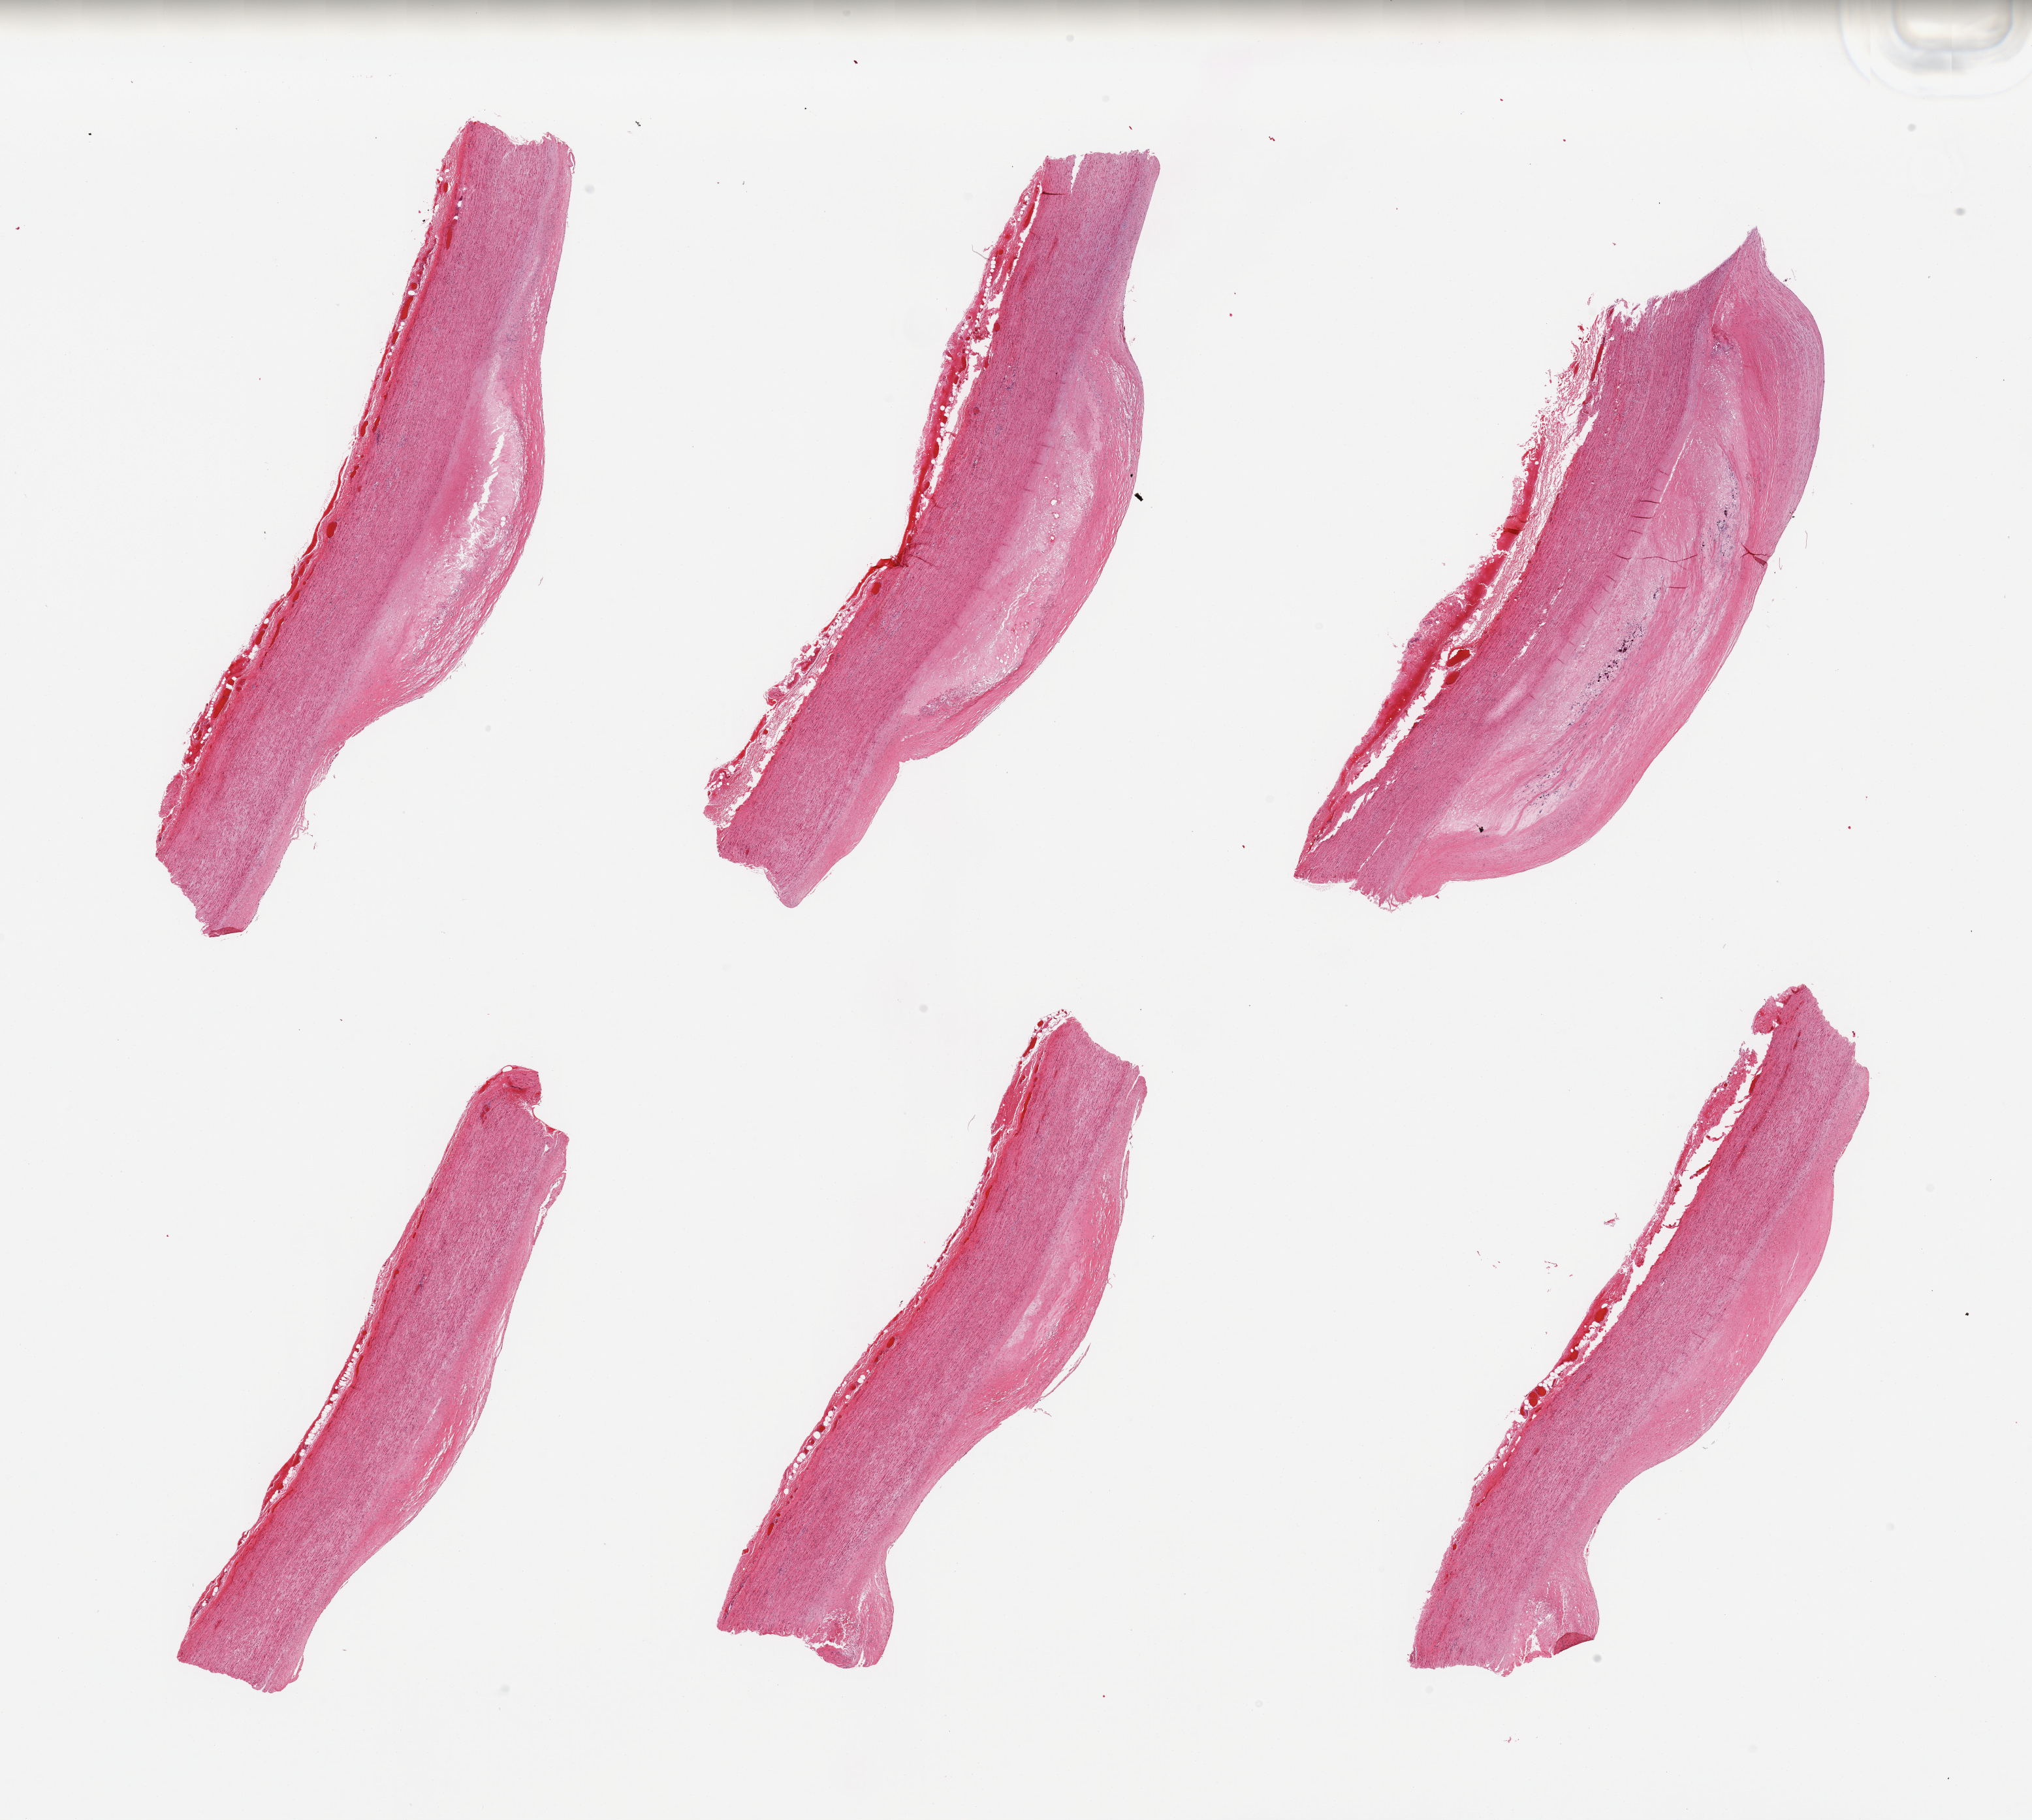
H&E whole-slide image, brightfield, low-resolution overview of the scanned area, about 24.6 x 22.0 mm; PAXgene-fixed, paraffin-embedded tissue; section of aorta (target tissue); tissue donor sample. Donor sex: male.
Pathologist's review note for this sample: 6 pieces; large atheromatous plaque occupies up to 60%.